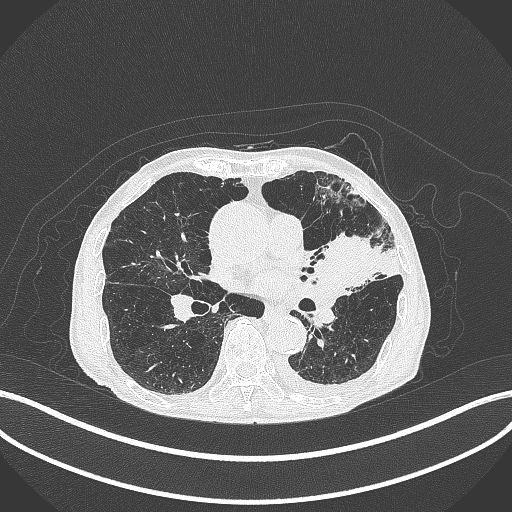
Chest CT, one axial slice; position 193 of 385 along the scan axis; 120 kVp; lung window (W 1500 / L -600 HU); 1 mm slice thickness; 512 × 512 image matrix, field of view 400 × 400 mm. Patient: male, 90 years or older. Case-level facts recorded for this patient, not image findings: clinical TNM (as recorded): T2b N1 M0.
Annotated regions visible in this slice (rectangle marked by the reading radiologist):
- lung tumour (recorded histology: squamous cell carcinoma): bounding box <315,225,376,292> (left, top, right, bottom; pixels)